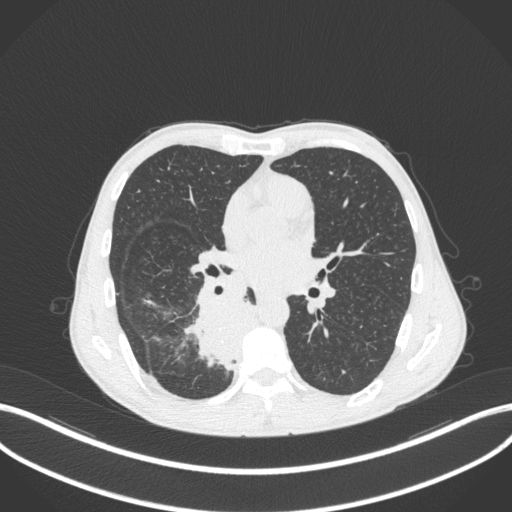
Chest CT, one axial slice. Slice 191 of 371 in the series (ordered by position). Lung window (W 1500 / L -600 HU). 1 mm slice thickness. 512 × 512 image matrix, field of view 400 × 400 mm. Male patient, age 58 years. Case-level facts recorded for this patient, not image findings: clinical TNM (as recorded): T3 N1 M1.
Structures marked on this image (rectangle marked by the reading radiologist):
- lung tumour (recorded histology: squamous cell carcinoma): bounding box <185,296,263,375> (left, top, right, bottom; pixels)